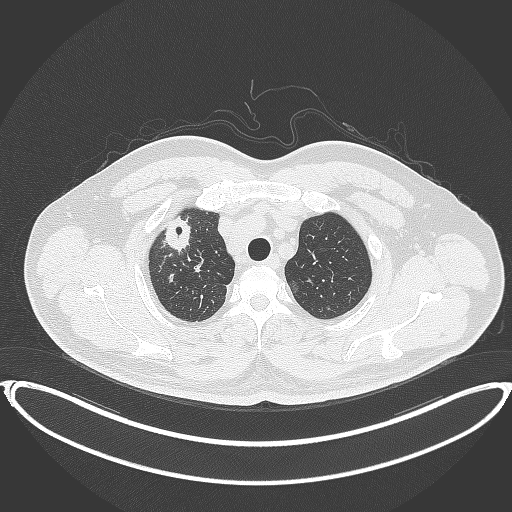
Chest CT, one axial slice. Slice 331 of 399 in the series (ordered by position). Reconstruction kernel B70f. 120 kVp. Lung window (W 1500 / L -600 HU). 512 × 512 image matrix. Patient: male, 53 years. Case-level facts recorded for this patient, not image findings: clinical TNM (as recorded): T2a N0 M0.
Structures marked on this image (rectangle marked by the reading radiologist):
- lung tumour (recorded histology: adenocarcinoma): bounding box <162,212,200,257> (left, top, right, bottom; pixels)